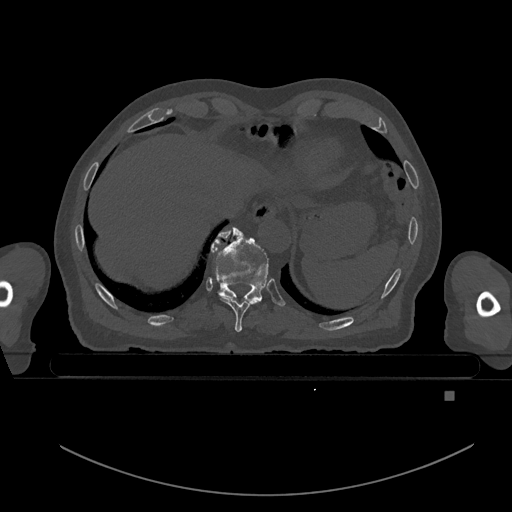
CT including the spine, one axial slice. Slice 117 of 969 in the series (ordered by position). Bone window (W 1800 / L 400 HU). 512 × 512 image matrix, field of view 456 × 456 mm. Male patient, age 82 years. From the clinical record (not read from this slice): primary cancer: prostate; vertebrae with lytic lesions (as recorded): T11, T9, T8, T2.
Outlined on this slice (semi-automatically segmented with operator editing):
- T10 vertebra: bounding box (x1, y1, x2, y2) in pixels: (211, 227, 269, 301)
- T9 vertebra: (218, 230, 261, 332)